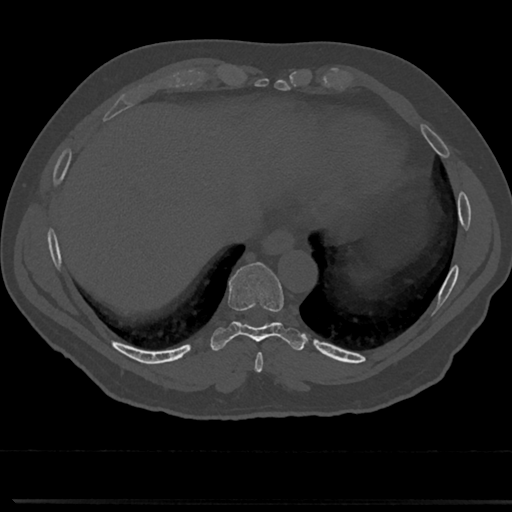
CT including the spine, one axial slice. Slice 304 of 817 in the series (ordered by position). Reconstruction kernel Br40s/3. 120 kVp. Bone window (W 1800 / L 400 HU). 0.5 mm slice thickness. 512 × 512 image matrix, field of view 355 × 355 mm. Patient: male, 61 years. From the clinical record (not read from this slice): primary cancer: prostate.
Outlined on this slice (semi-automatically segmented with operator editing):
- T8 vertebra: box from (x=233, y=306) to (x=286, y=355) px
- T9 vertebra: (x=232, y=266)–(x=283, y=329)